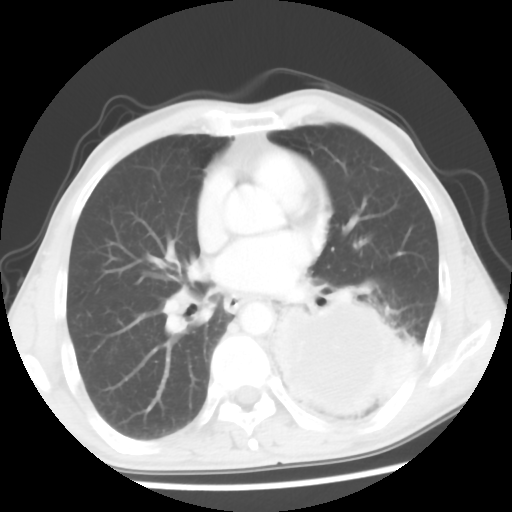
Chest CT, one axial slice. Position 28 of 56 along the scan axis. 120 kVp. Lung window (W 1500 / L -600 HU). 5 mm slice thickness. 512 × 512 image matrix, field of view 318 × 318 mm. Male patient, age 60 years. From the clinical record (not read from this slice): clinical TNM (as recorded): T4 N0 M0.
Annotated regions visible in this slice (bounding box drawn by a radiologist):
- lung tumour (recorded histology: squamous cell carcinoma): bounding box (x1, y1, x2, y2) in pixels: (263, 286, 416, 422)